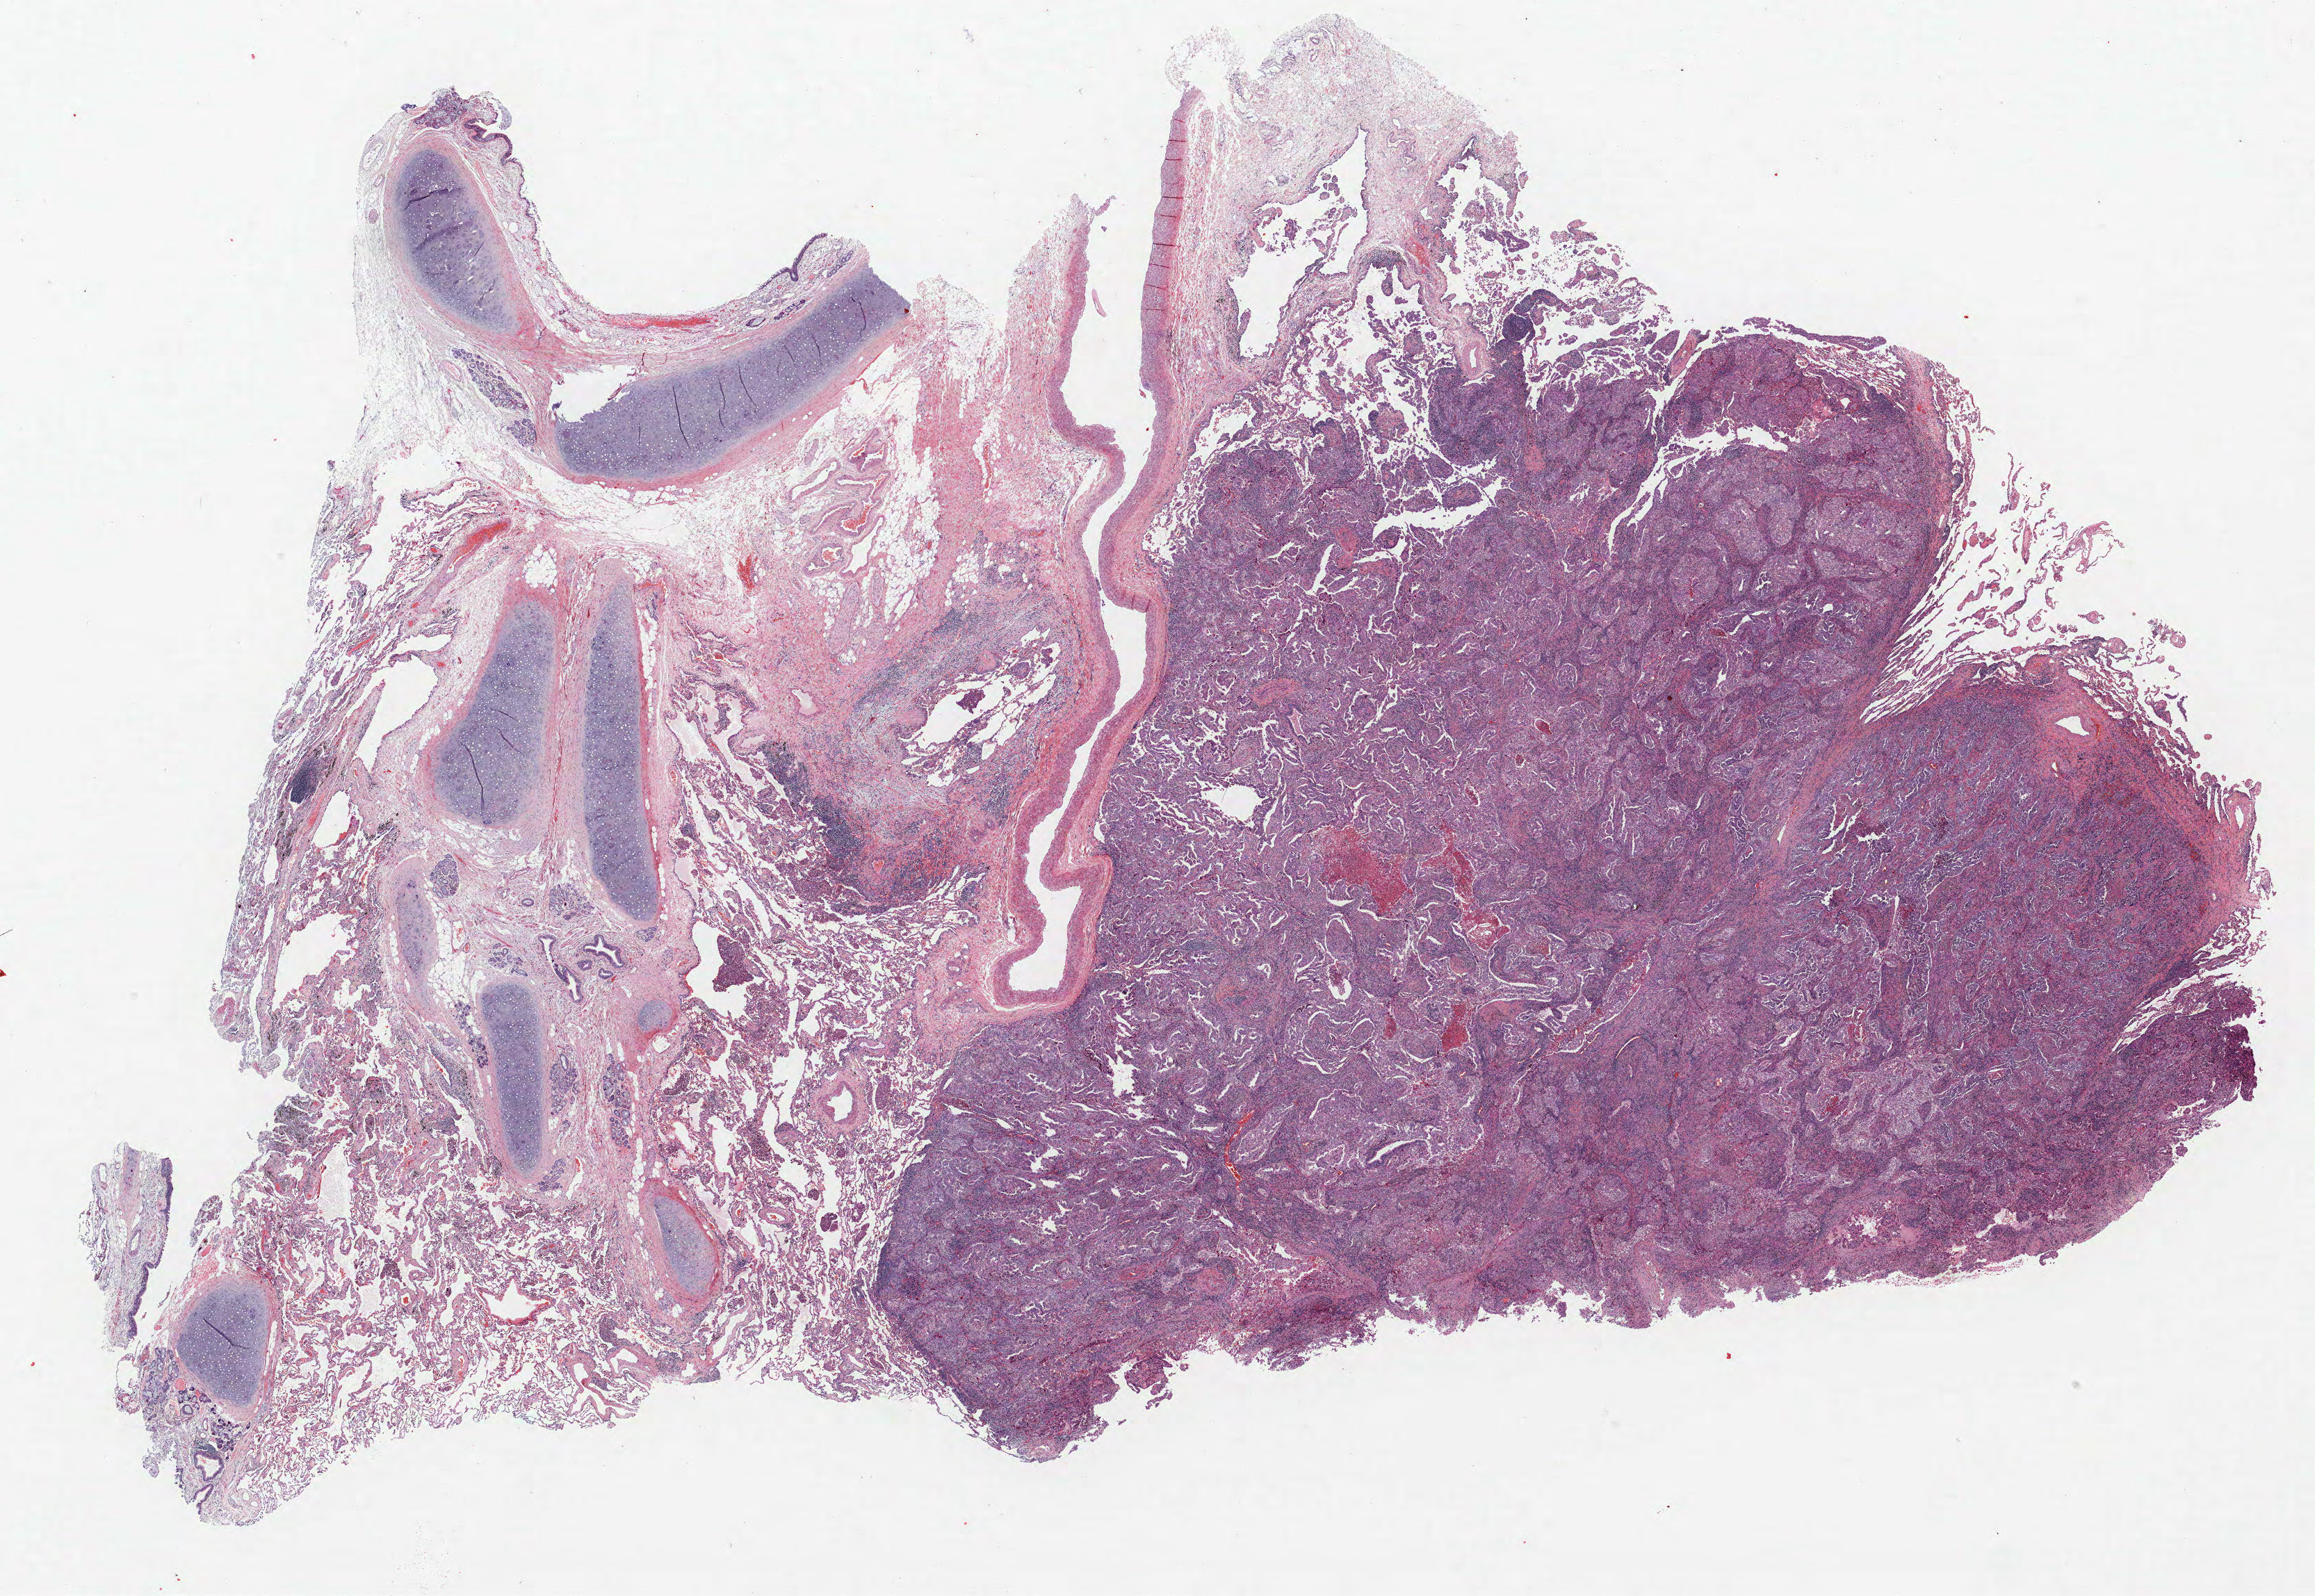
Whole-slide histology image, H&E-stained, whole scanned area (about 26.6 x 18.4 mm) shown as a low-resolution overview, formalin-fixed paraffin-embedded (FFPE) section, lung tissue. Male patient, aged 59 at enrolment. Current smoker at enrolment. Grade: poorly differentiated (G3).
Primary tumour location (clinical record): right upper lobe. Tumour size (pathology): 34 mm. Participant's lung-cancer diagnosis: Large cell carcinoma, NOS. Stage (AJCC 6th edition): IIIA.